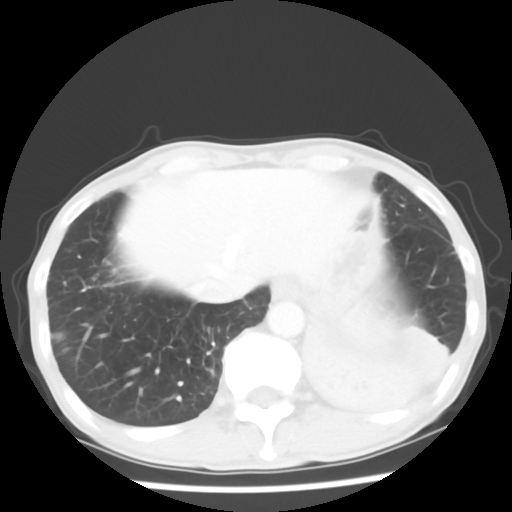
Chest CT, one axial slice; slice 10 of 64 in the series (ordered by position); reconstruction kernel STANDARD; 120 kVp; lung window (W 1500 / L -600 HU); 512 × 512 image matrix. Male patient, age 68 years. From the clinical record (not read from this slice): clinical TNM (as recorded): T4 N0 M0.
Annotated regions visible in this slice (rectangle marked by the reading radiologist):
- lung tumour (recorded histology: squamous cell carcinoma): bounding box <291,301,471,436> (left, top, right, bottom; pixels)